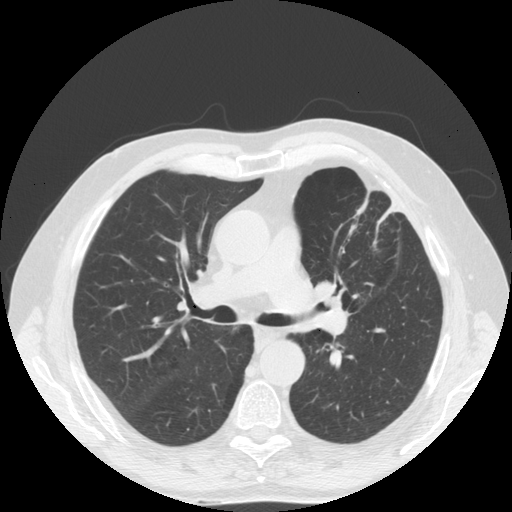
Low-dose screening chest CT, one axial slice. Slice 108 of 170 in the series (ordered by position). 140 kVp. Lung window (W 1500 / L -600 HU). 512 × 512 image matrix, field of view 380 × 380 mm.
Structures marked on this image (manually delineated by an expert):
- lesion 1 (tumor, upper lobe of left lung): bounding box (x1, y1, x2, y2) in pixels: (314, 281, 335, 299)